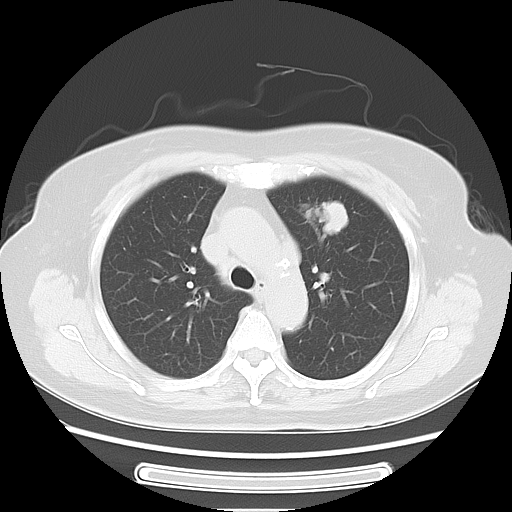
Chest CT, one axial slice. Position 43 of 57 along the scan axis. Lung window (W 1500 / L -600 HU). 5 mm slice thickness. 512 × 512 image matrix, field of view 363 × 363 mm. Female patient, age 77 years. Case-level facts recorded for this patient, not image findings: clinical TNM (as recorded): T1c N3 M0.
Outlined on this slice (rectangle marked by the reading radiologist):
- lung tumour (recorded histology: adenocarcinoma): bounding box [x1, y1, x2, y2] px = [296, 194, 363, 246]